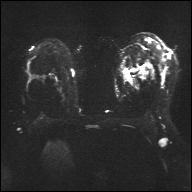
Breast MRI, one axial slice; position 24 of 32 along the scan axis; diffusion-weighted series; image 2 of 4 stored at this slice position (different b-values; order by instance number); 1.5 T; 192 × 192 image matrix, field of view 360 × 360 mm. Female patient.
Annotated regions visible in this slice (expert manual segmentation):
- tumour on diffusion-weighted imaging: bounding box [x1, y1, x2, y2] px = [139, 71, 144, 78]